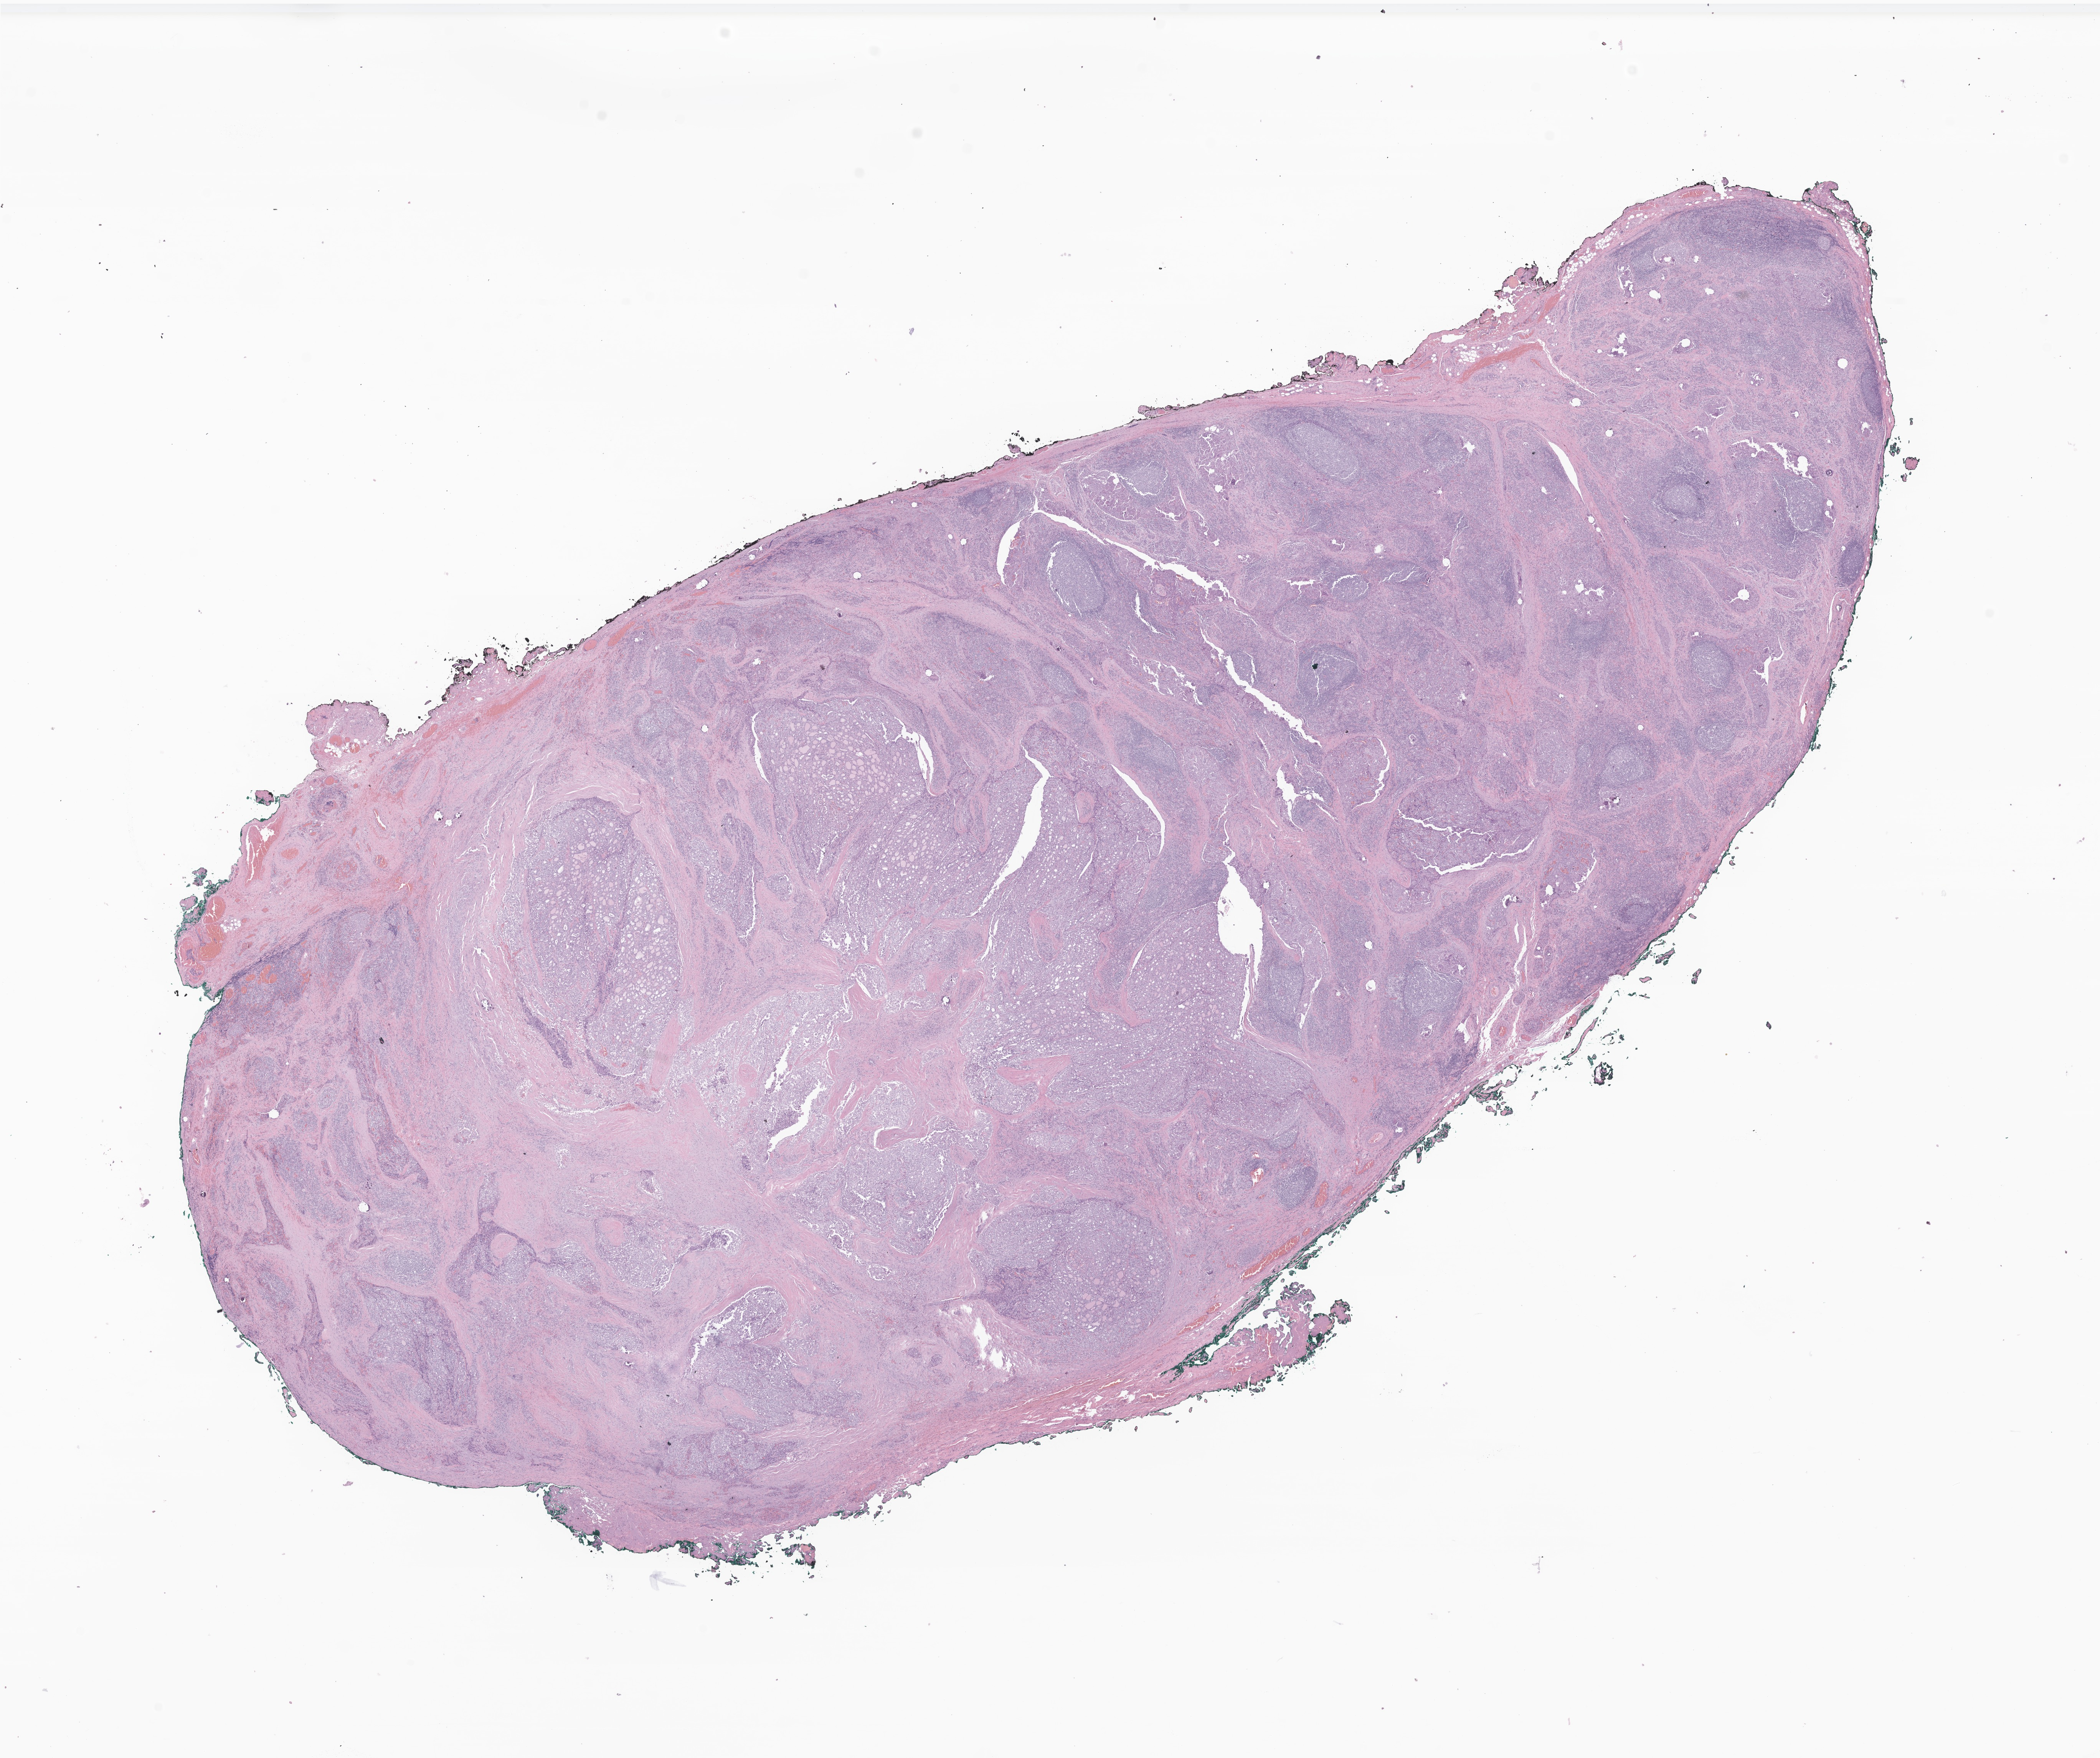
H&E whole-slide image of tumor tissue from the thyroid — low-resolution overview of the scanned area, about 23.1 x 19.3 mm. Formalin-fixed, paraffin-embedded (FFPE) tissue. Patient: male, age 68 months (5 years 8 months).
Diagnosis: Papillary carcinoma, NOS.